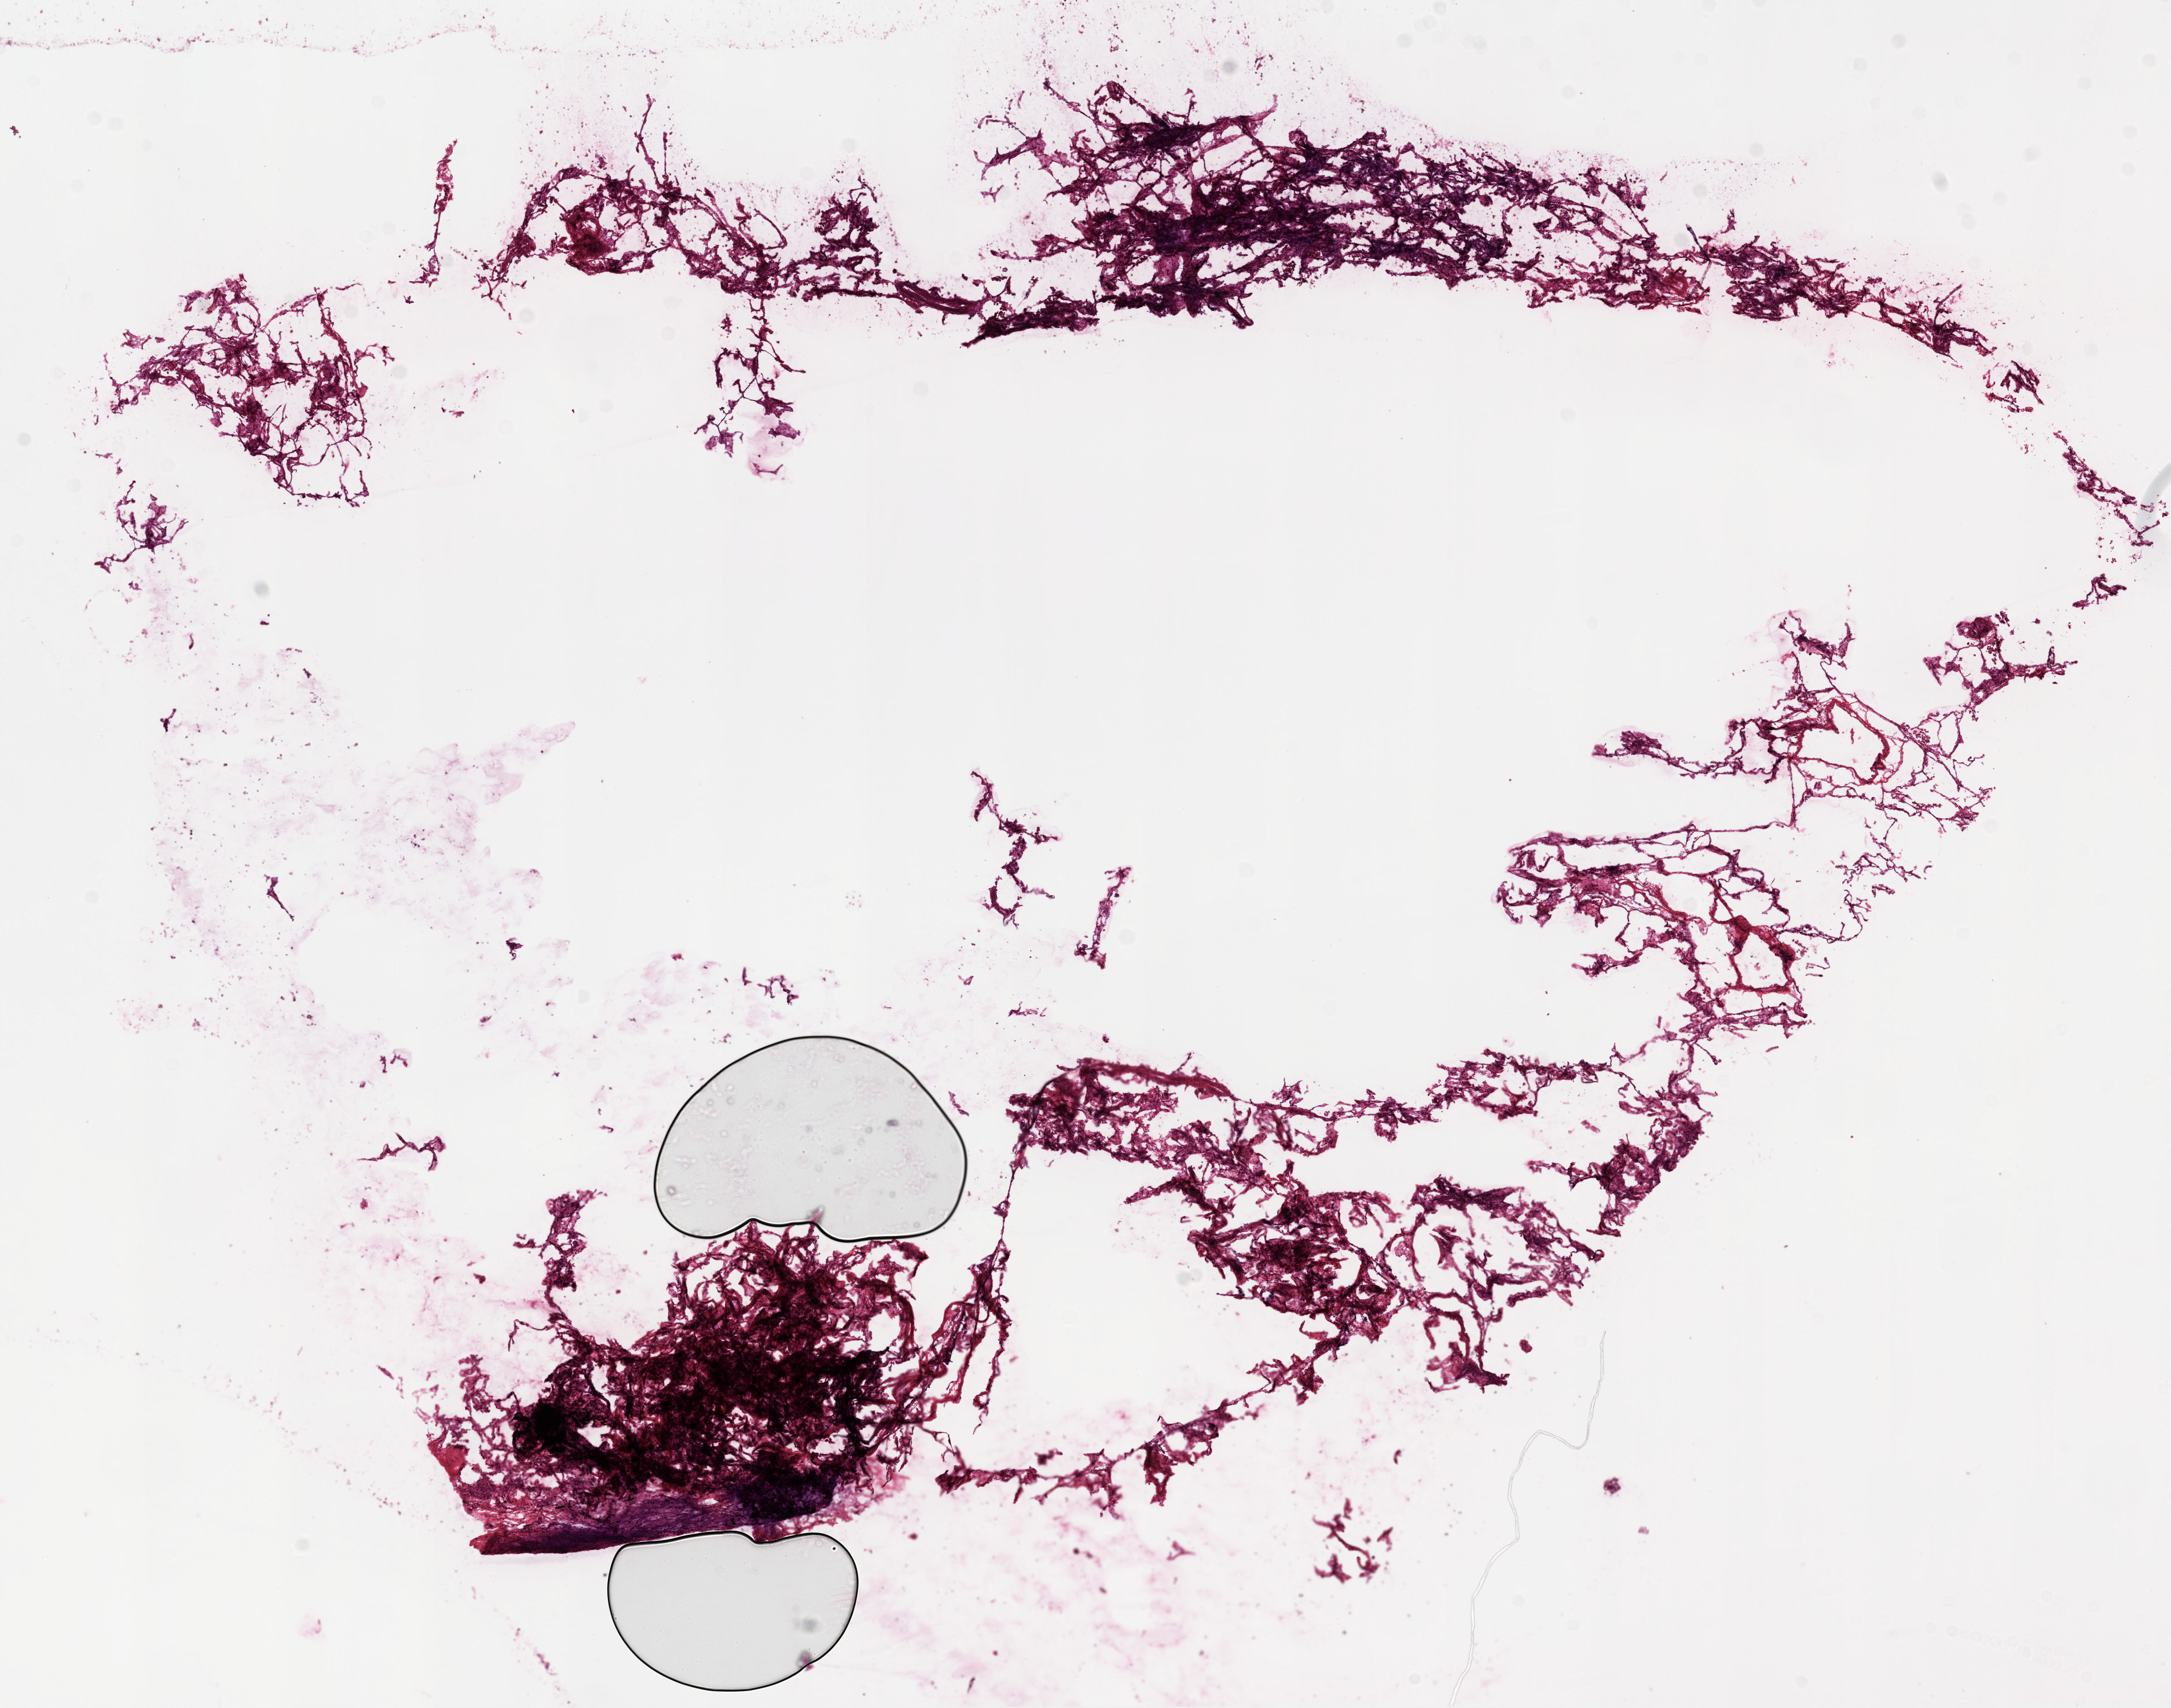
Hematoxylin and eosin (H&E) stained whole-slide image — low-resolution overview of the scanned area, about 15.0 x 11.8 mm; frozen section from the top of the tissue portion; solid tissue normal (non-tumour tissue) sample from the lung. Female patient; age at initial diagnosis 81 years.
- this section: solid tissue normal sample (biorepository sample class)
- patient diagnosis: Squamous cell carcinoma, NOS (lower lobe, lung)